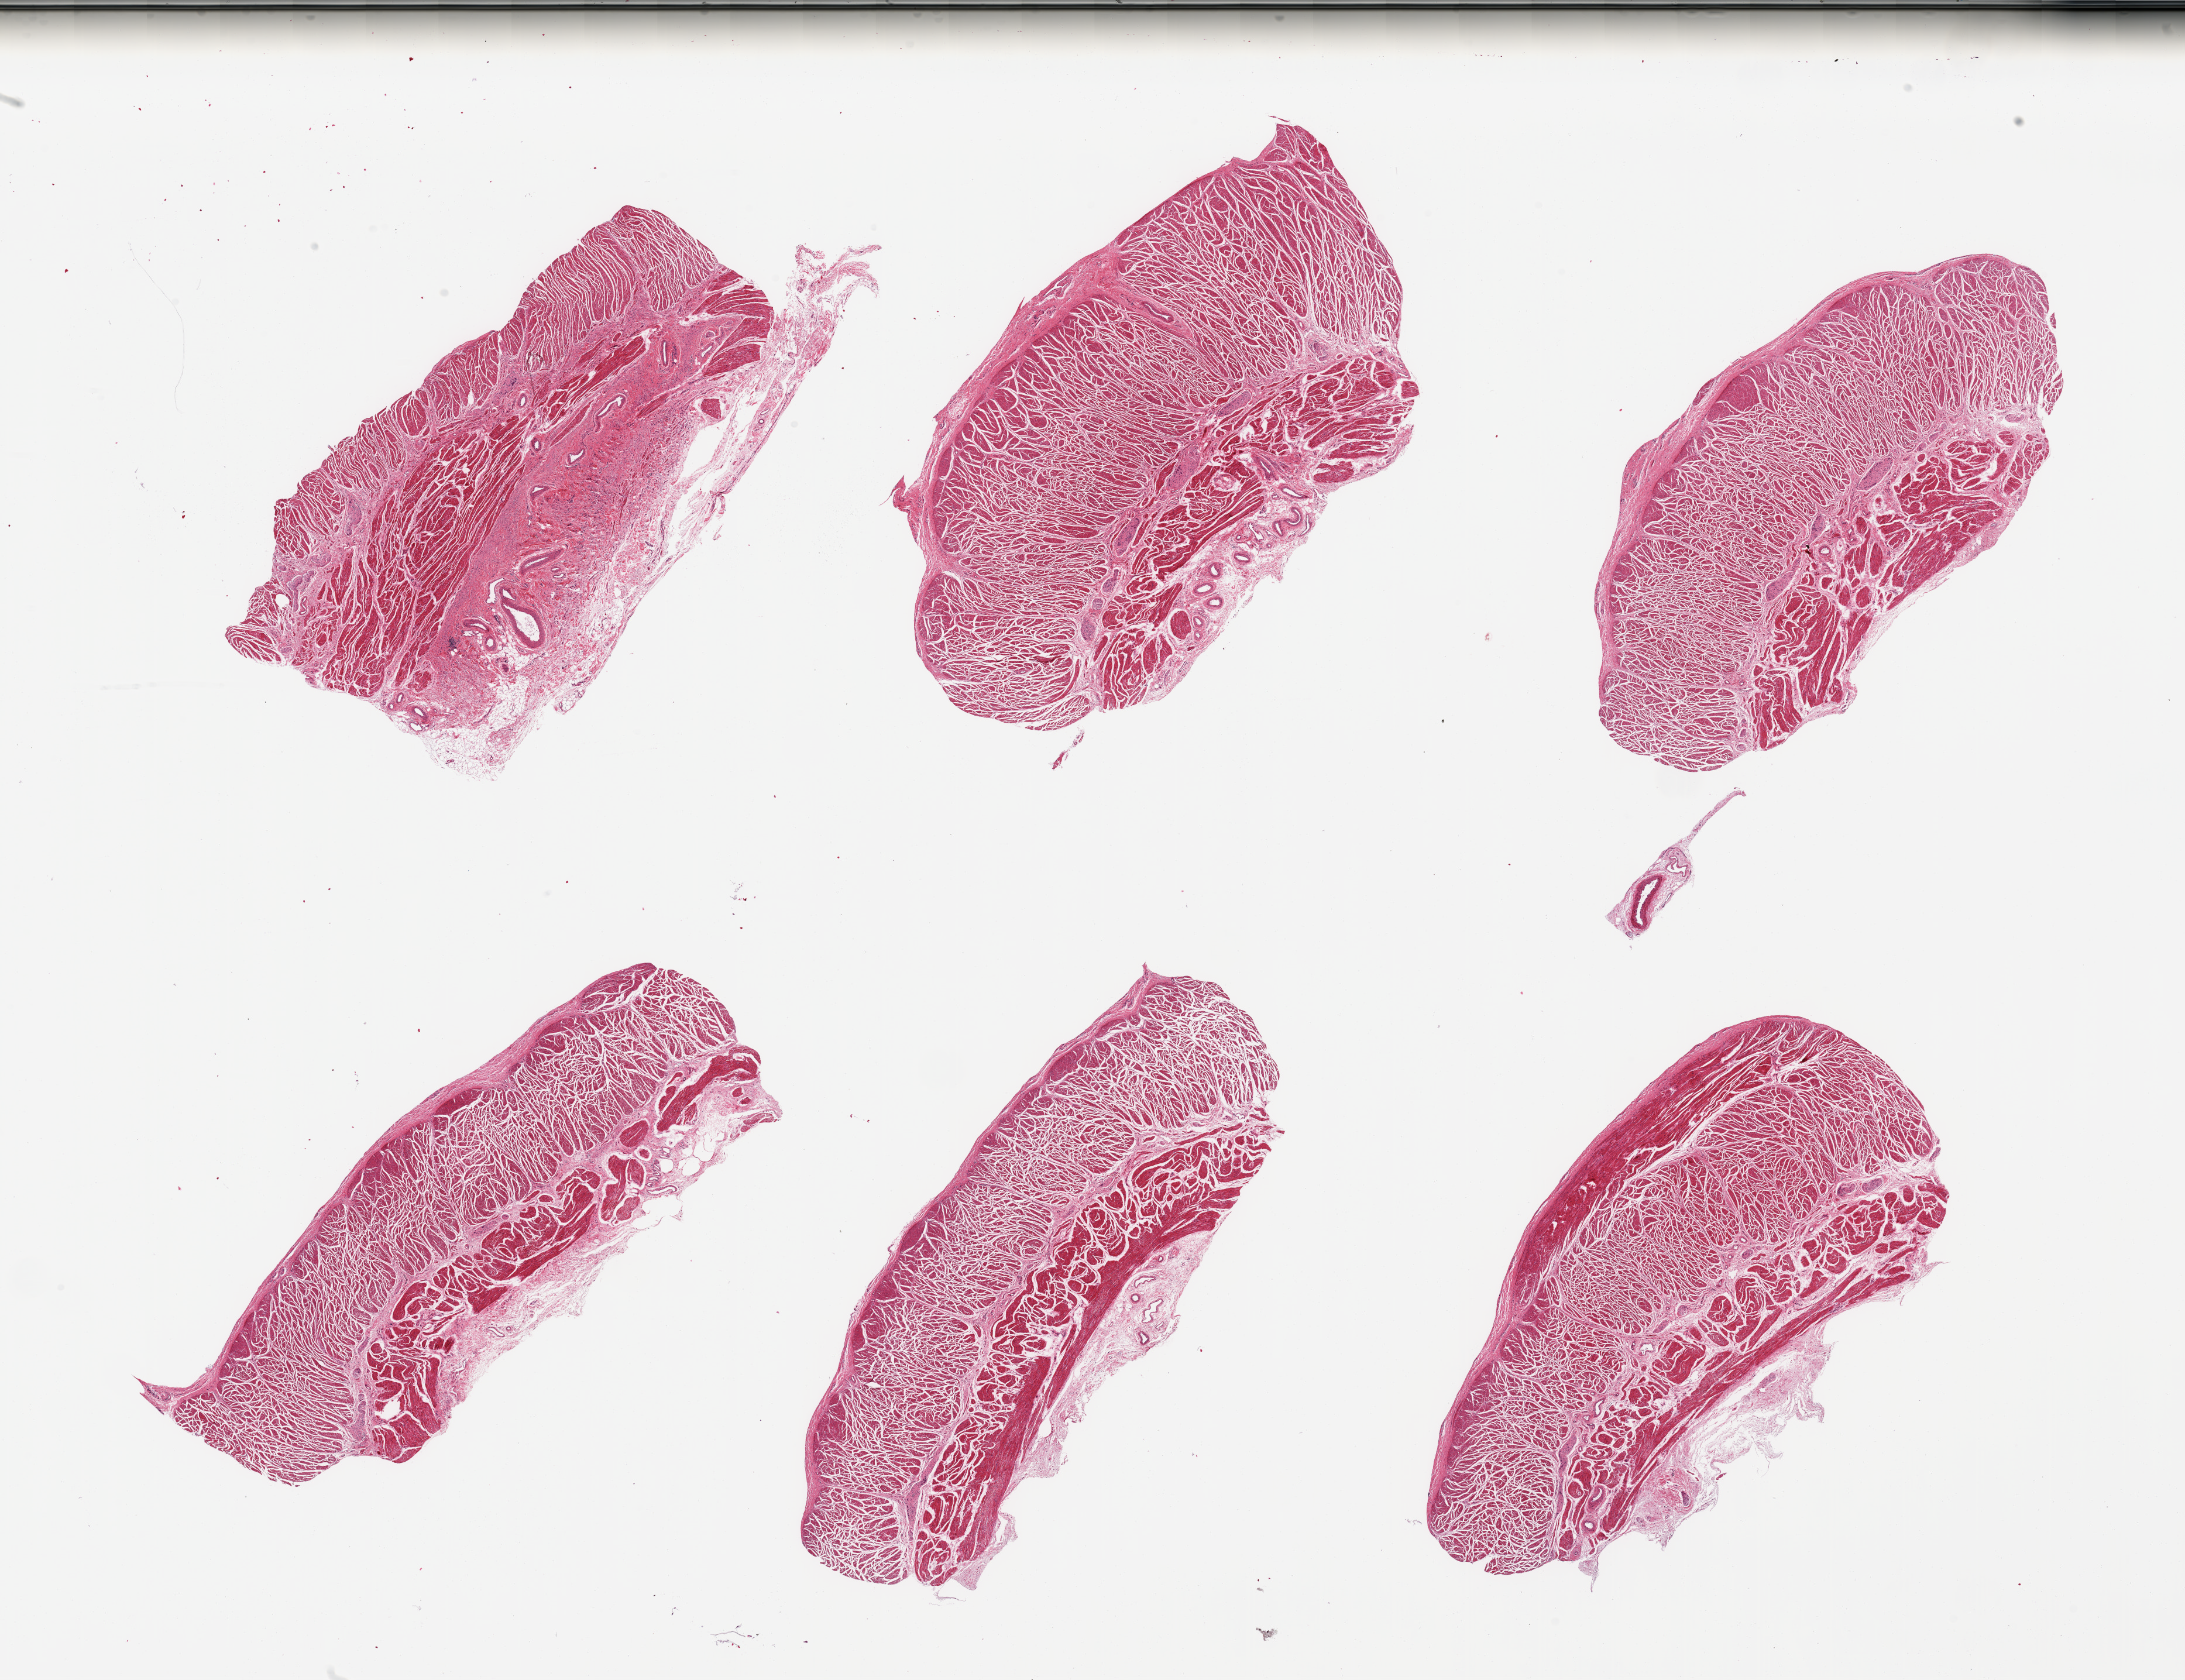
Digitized haematoxylin and eosin-stained section, brightfield — whole scanned area (about 29.5 x 22.7 mm) shown as a low-resolution overview, PAXgene-fixed, paraffin-embedded tissue, section of esophageal muscle (target tissue), donor tissue sample.
Reviewer comment on this tissue sample: 6 pieces; well dissected muscularis except for a 50% fibrous submucosa in 1 piece.